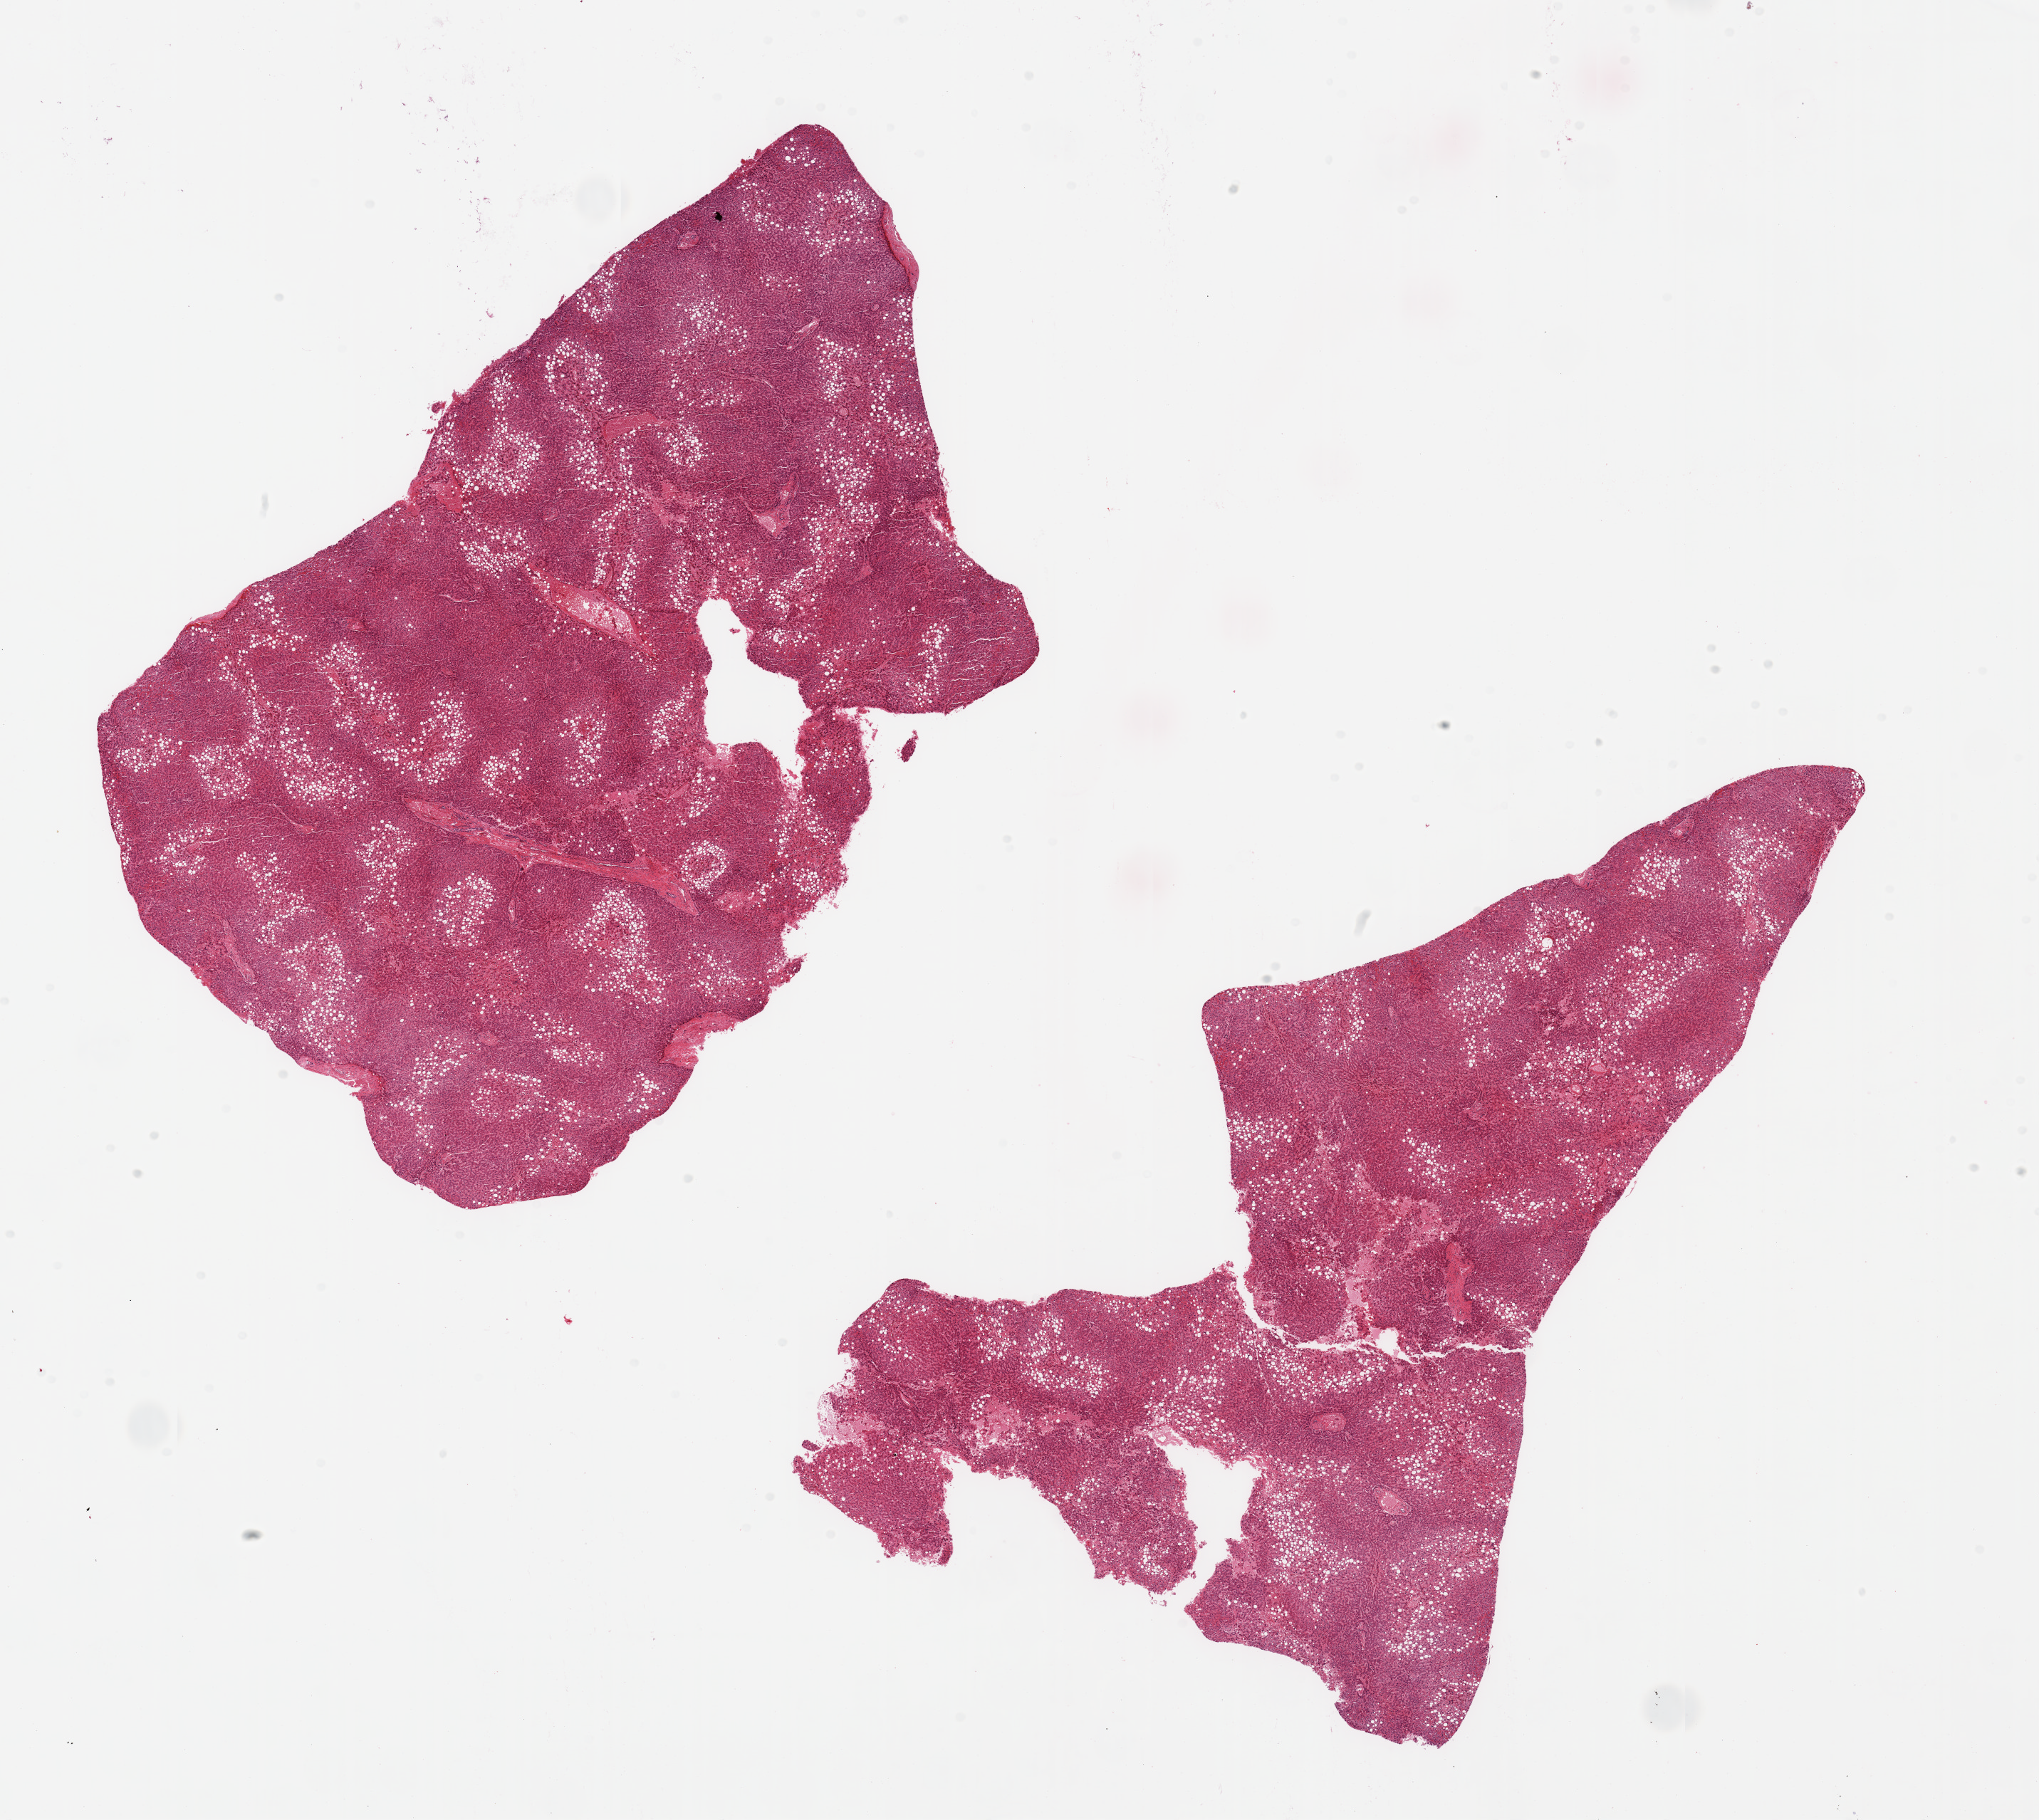
Whole-slide image, hematoxylin and eosin (H&E) stain — a low-resolution overview of the entire scanned area, about 22.6 x 20.2 mm. PAXgene-fixed, paraffin-embedded tissue. Sampled site (target tissue): liver. Donor tissue sample.
Review note (as recorded): 2 pieces; congestion, moderate steatosis.